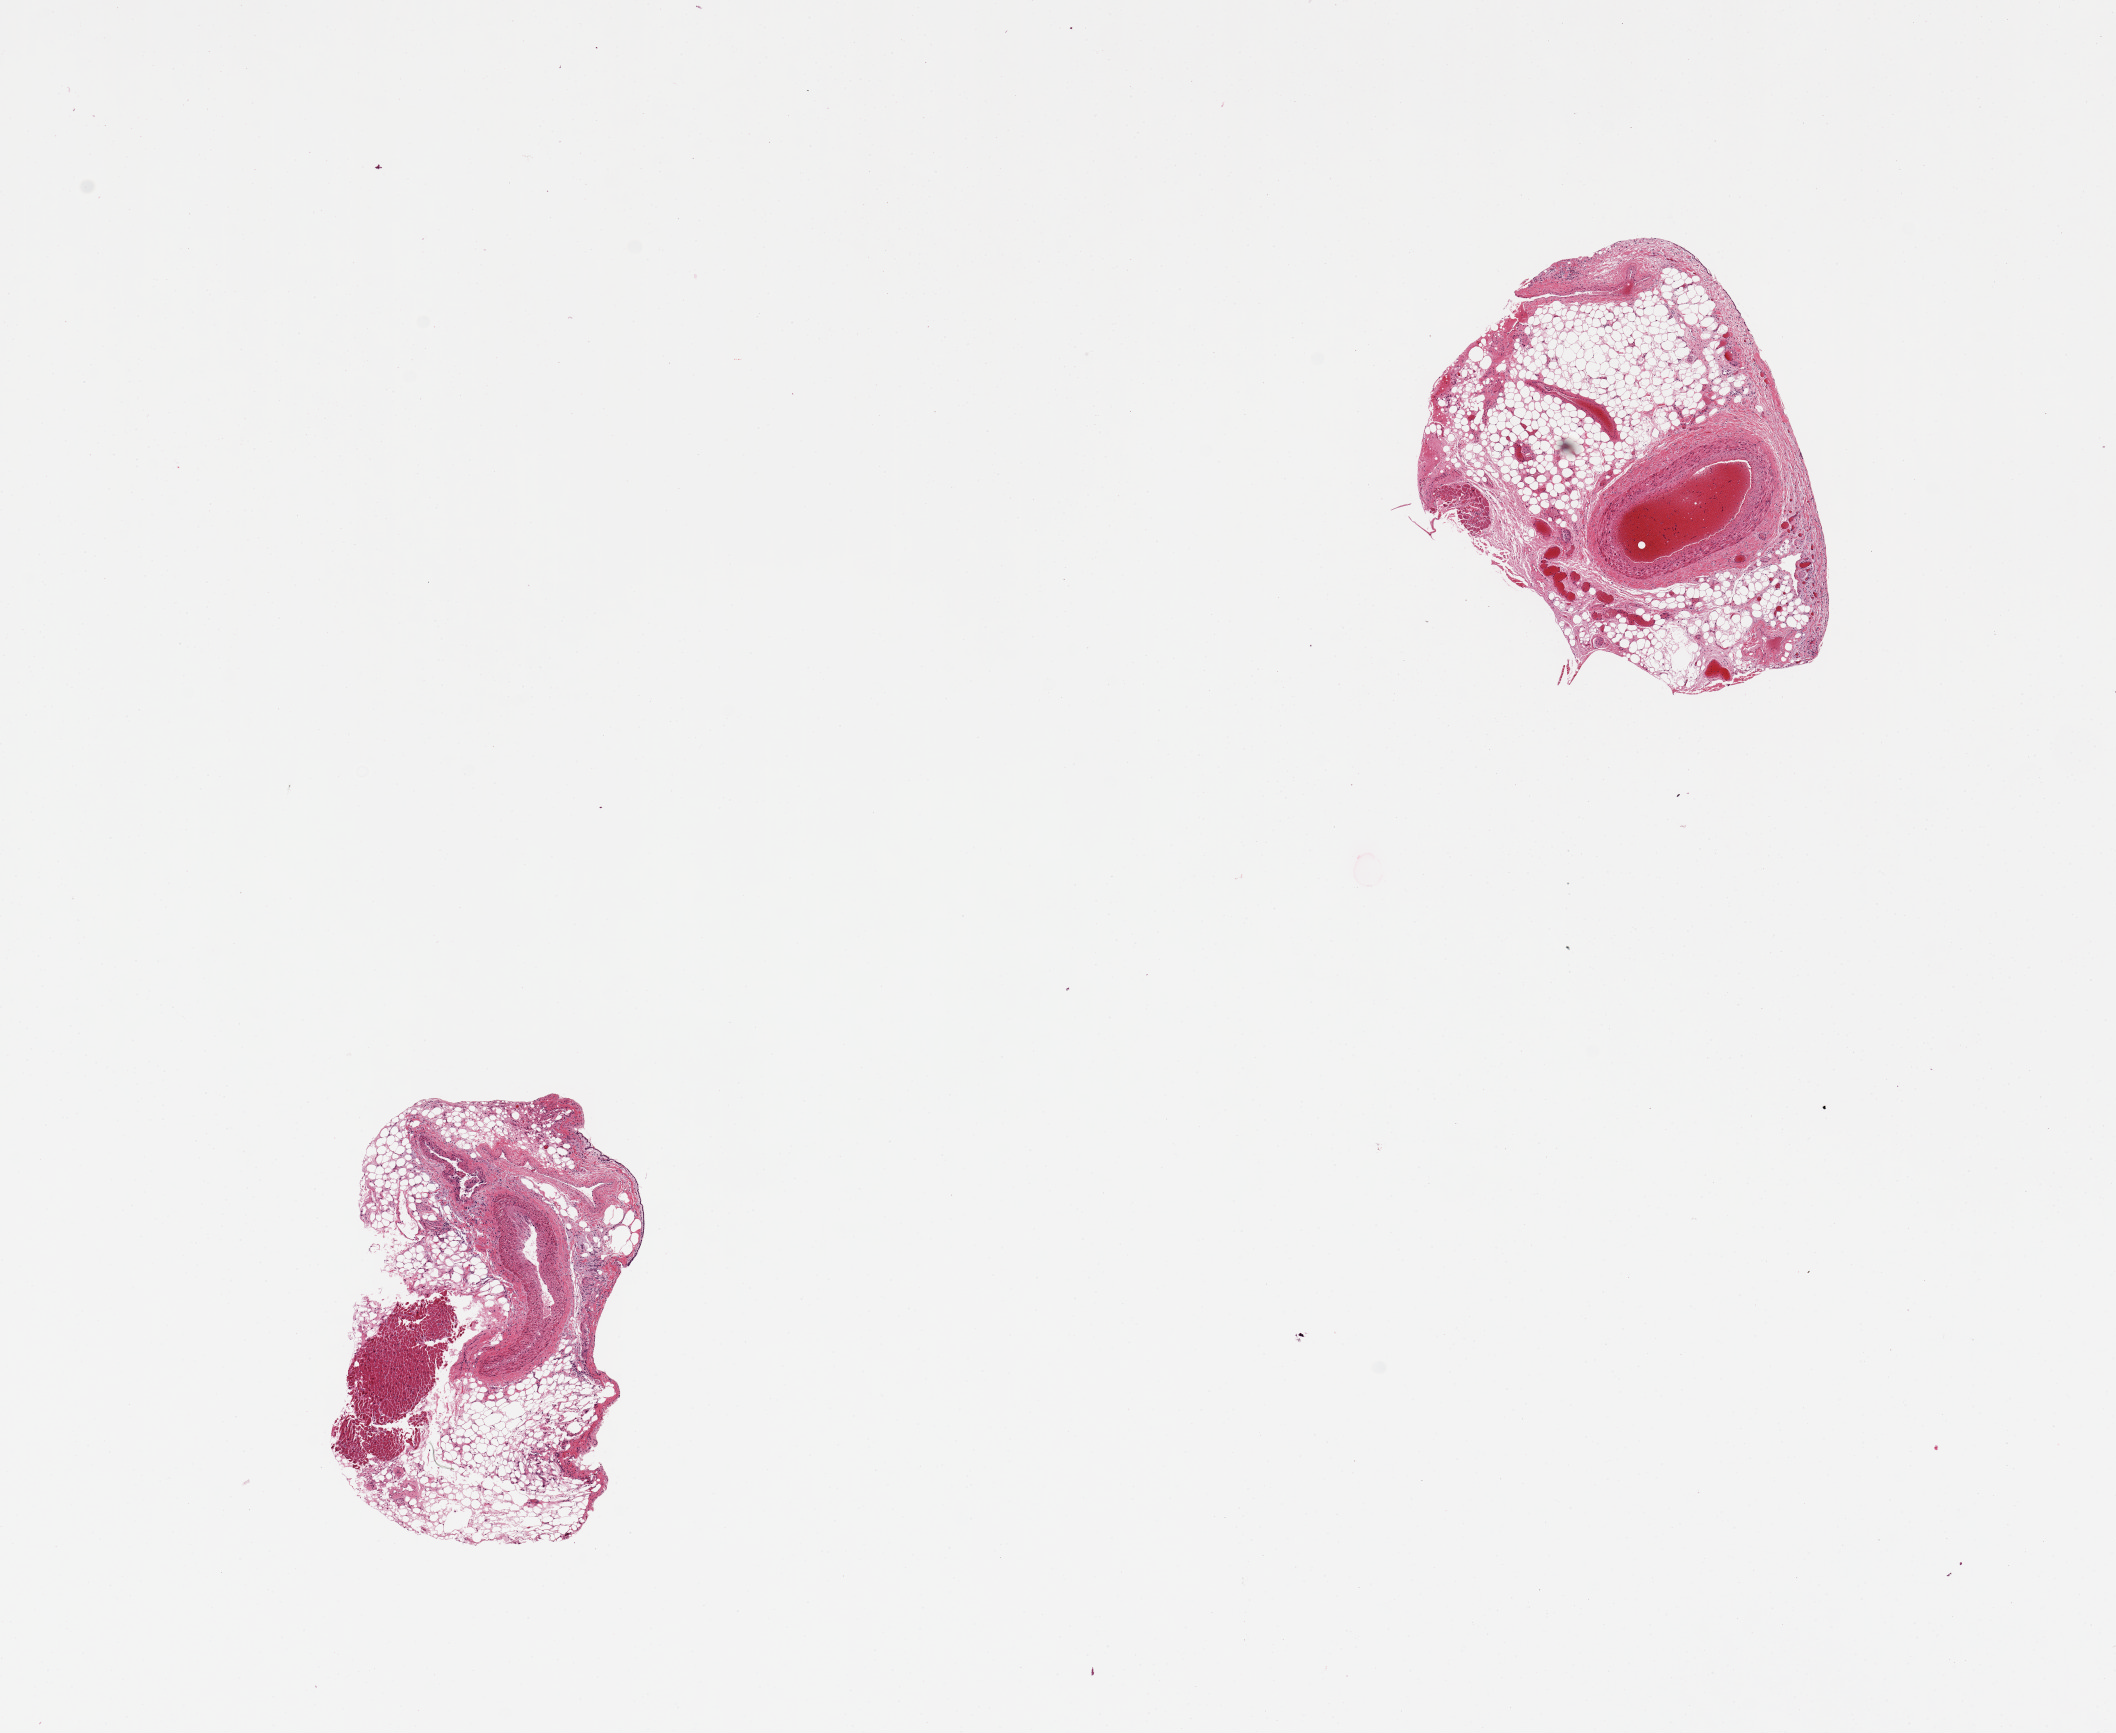
Hematoxylin and eosin (H&E) whole-slide image, shown as a low-resolution overview of the whole scanned area (about 16.7 x 13.7 mm, acquisition: 20x scan), PAXgene-fixed, paraffin-embedded tissue, section of coronary artery (target tissue), donor tissue sample. Donor sex: female.
Pathologist's review note for this sample: 2 pieces, vessel represents ~20% of each piece, abundant attached fat and myocardium.